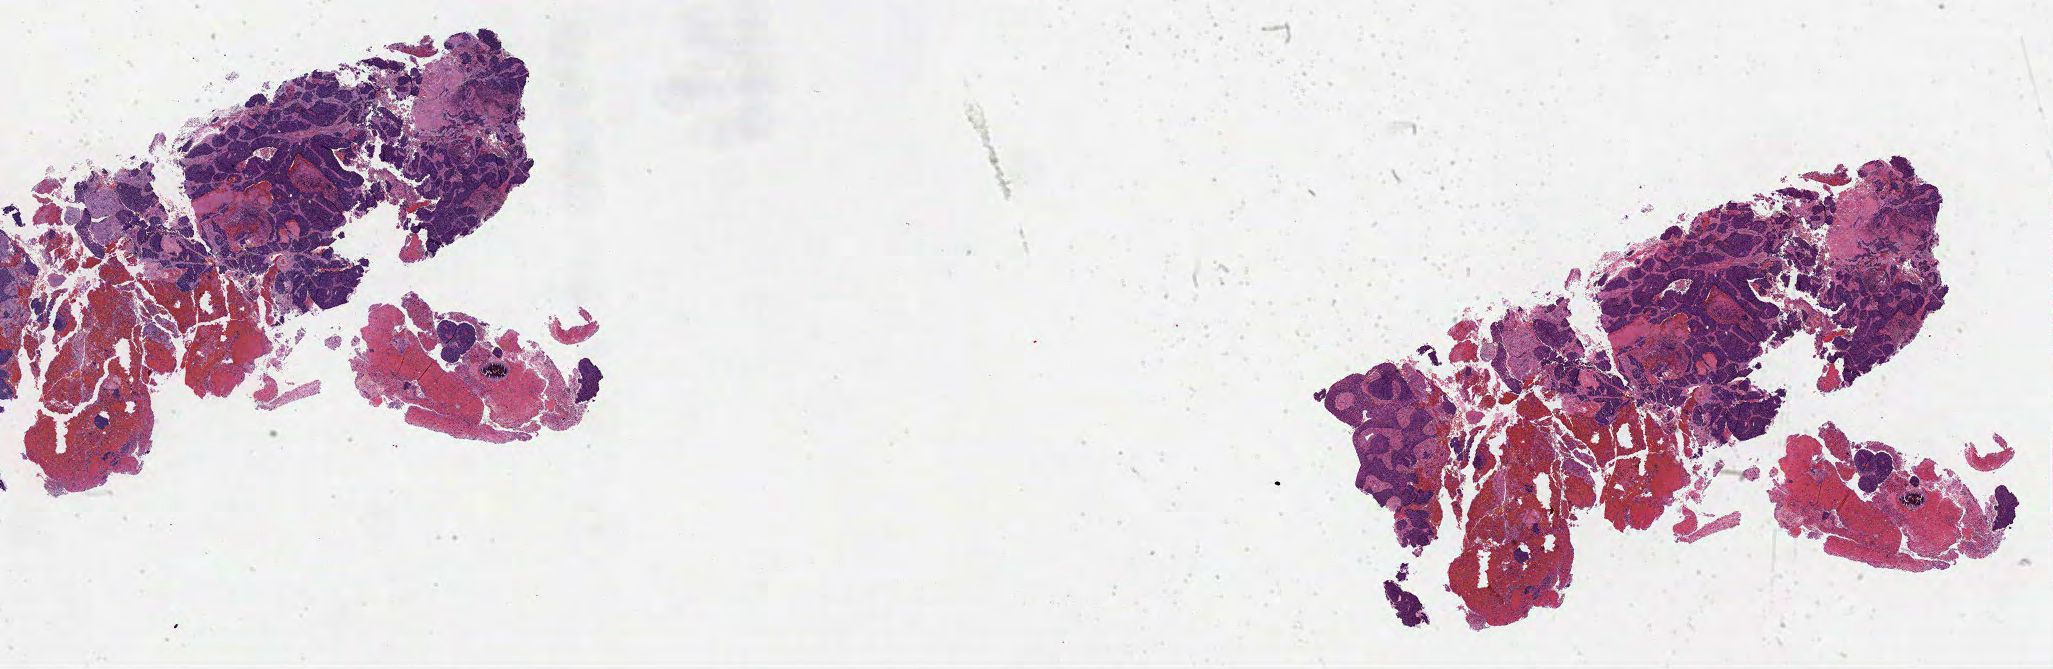
Digitized H&E tissue section (whole slide) — whole scanned area (about 33.1 x 10.8 mm) shown as a low-resolution overview. Formalin-fixed paraffin-embedded (FFPE) diagnostic section. Sample: primary tumour, lung. Male, age 70 years at initial diagnosis.
Pathologic diagnosis: Basaloid squamous cell carcinoma (lower lobe, lung). AJCC pathologic stage: IB.